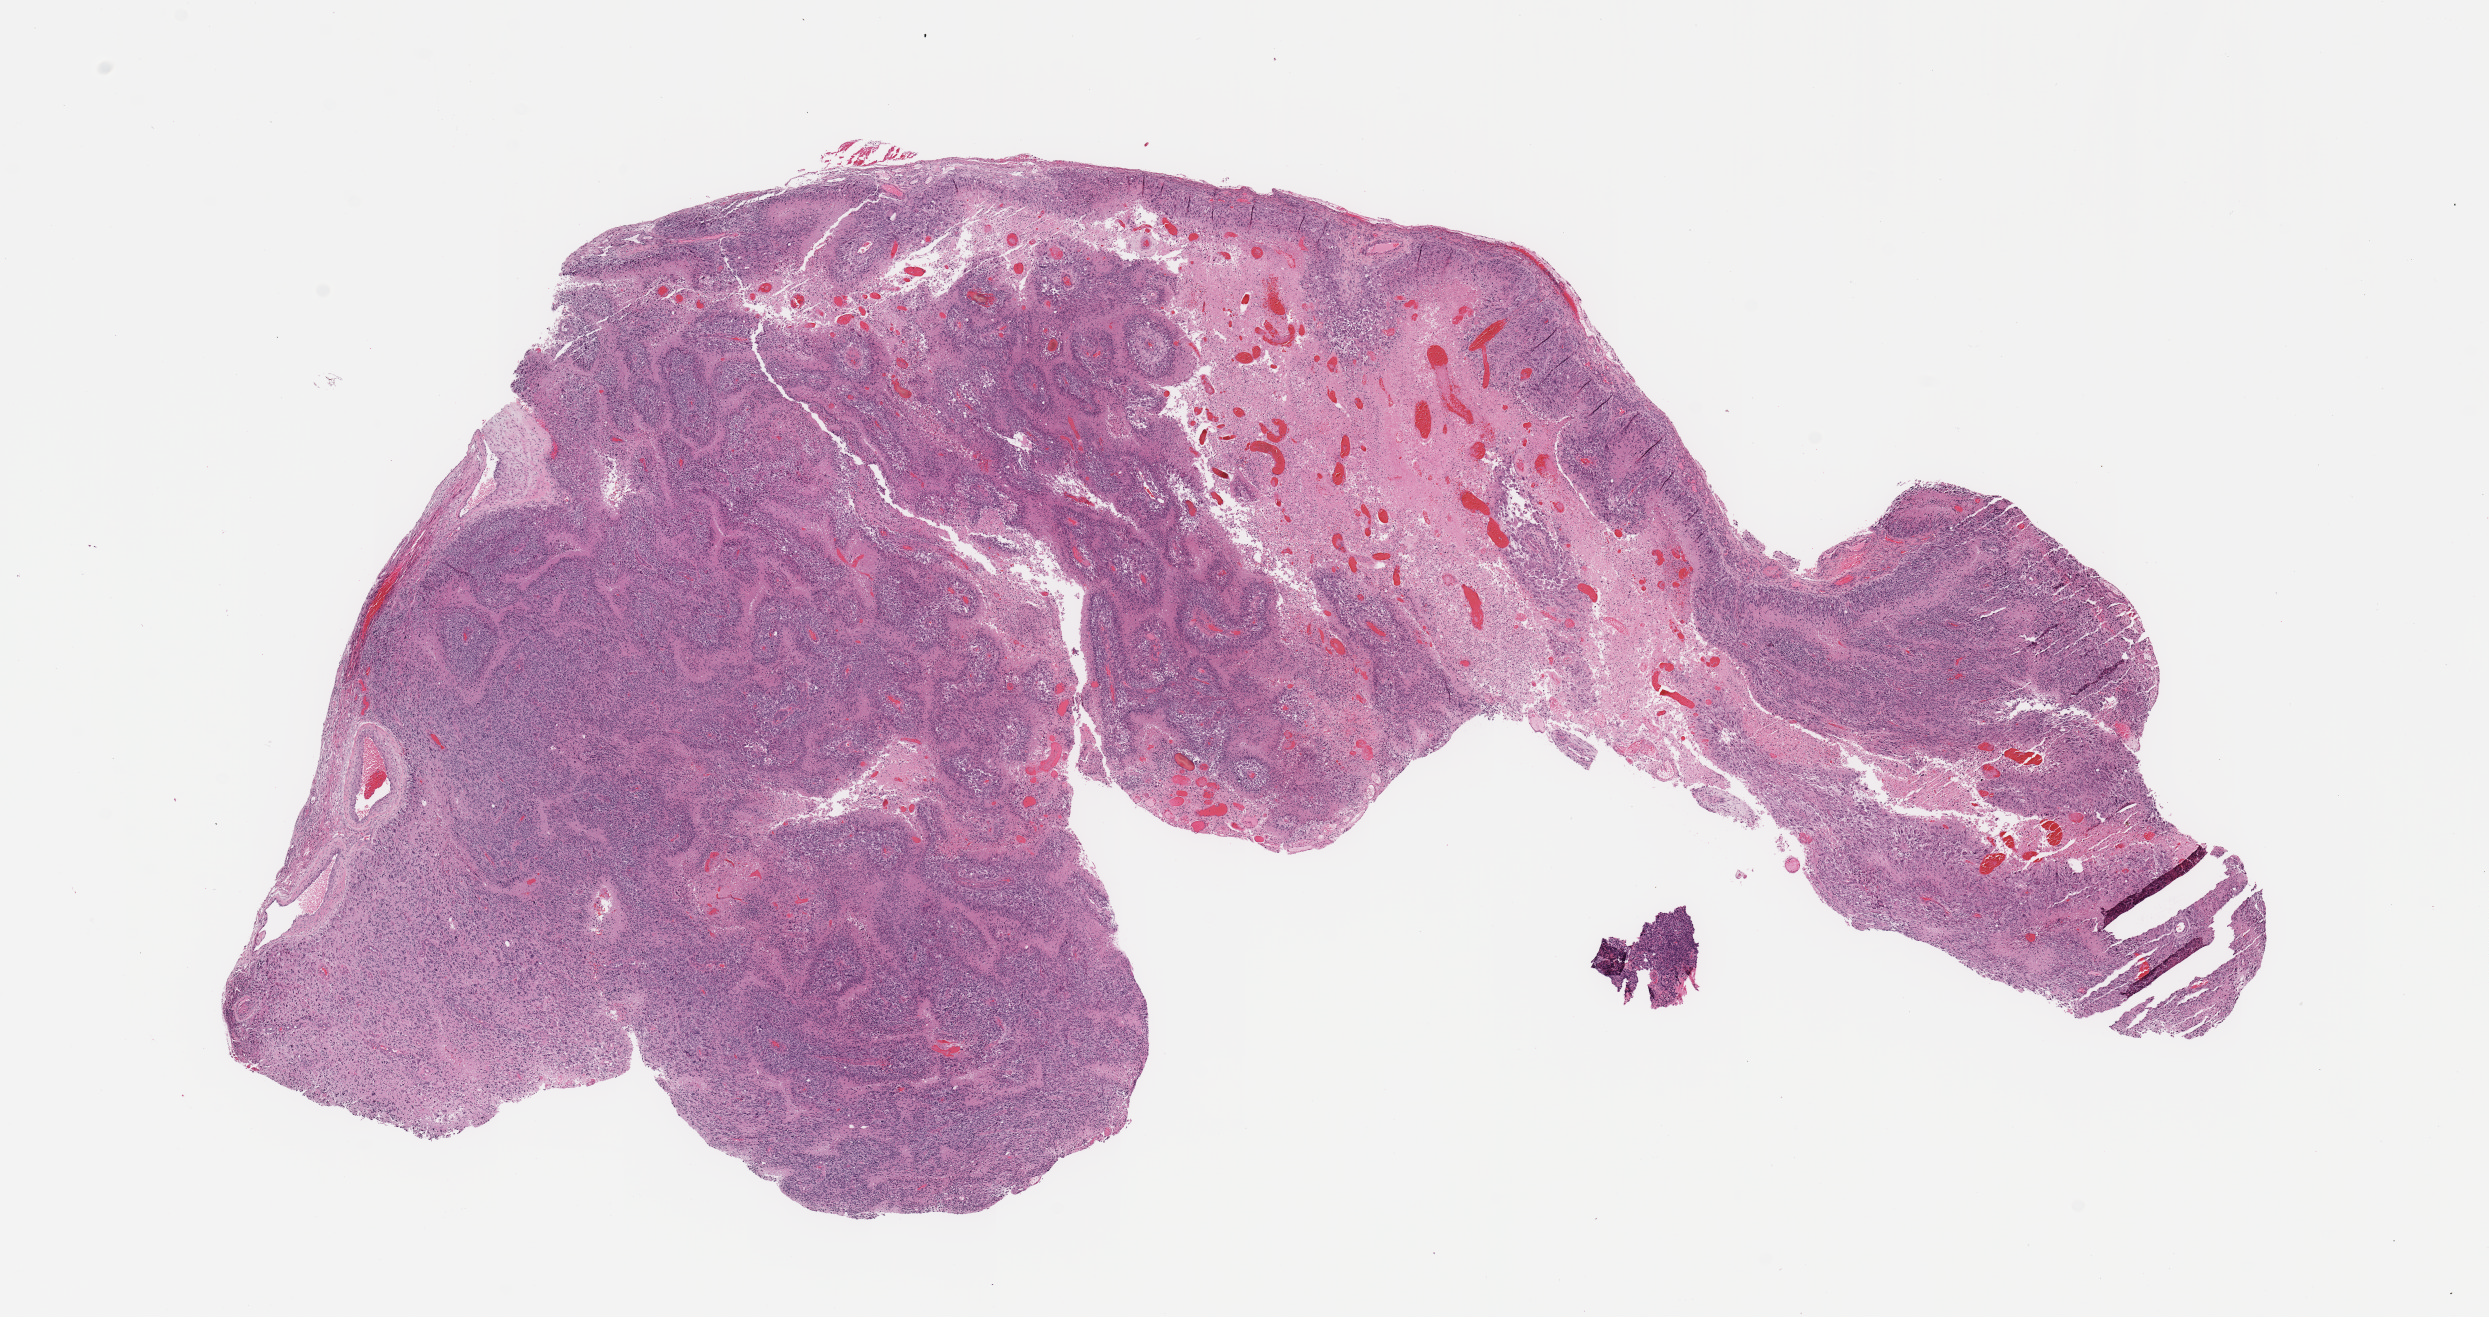
Hematoxylin and eosin (H&E) stained whole-slide image — low-resolution overview of the scanned area, about 19.7 x 10.4 mm (acquisition: 20x scan); tumour tissue sample, sampled site: brain. Patient: female, age 51 years.
Diagnosis: Glioblastoma.